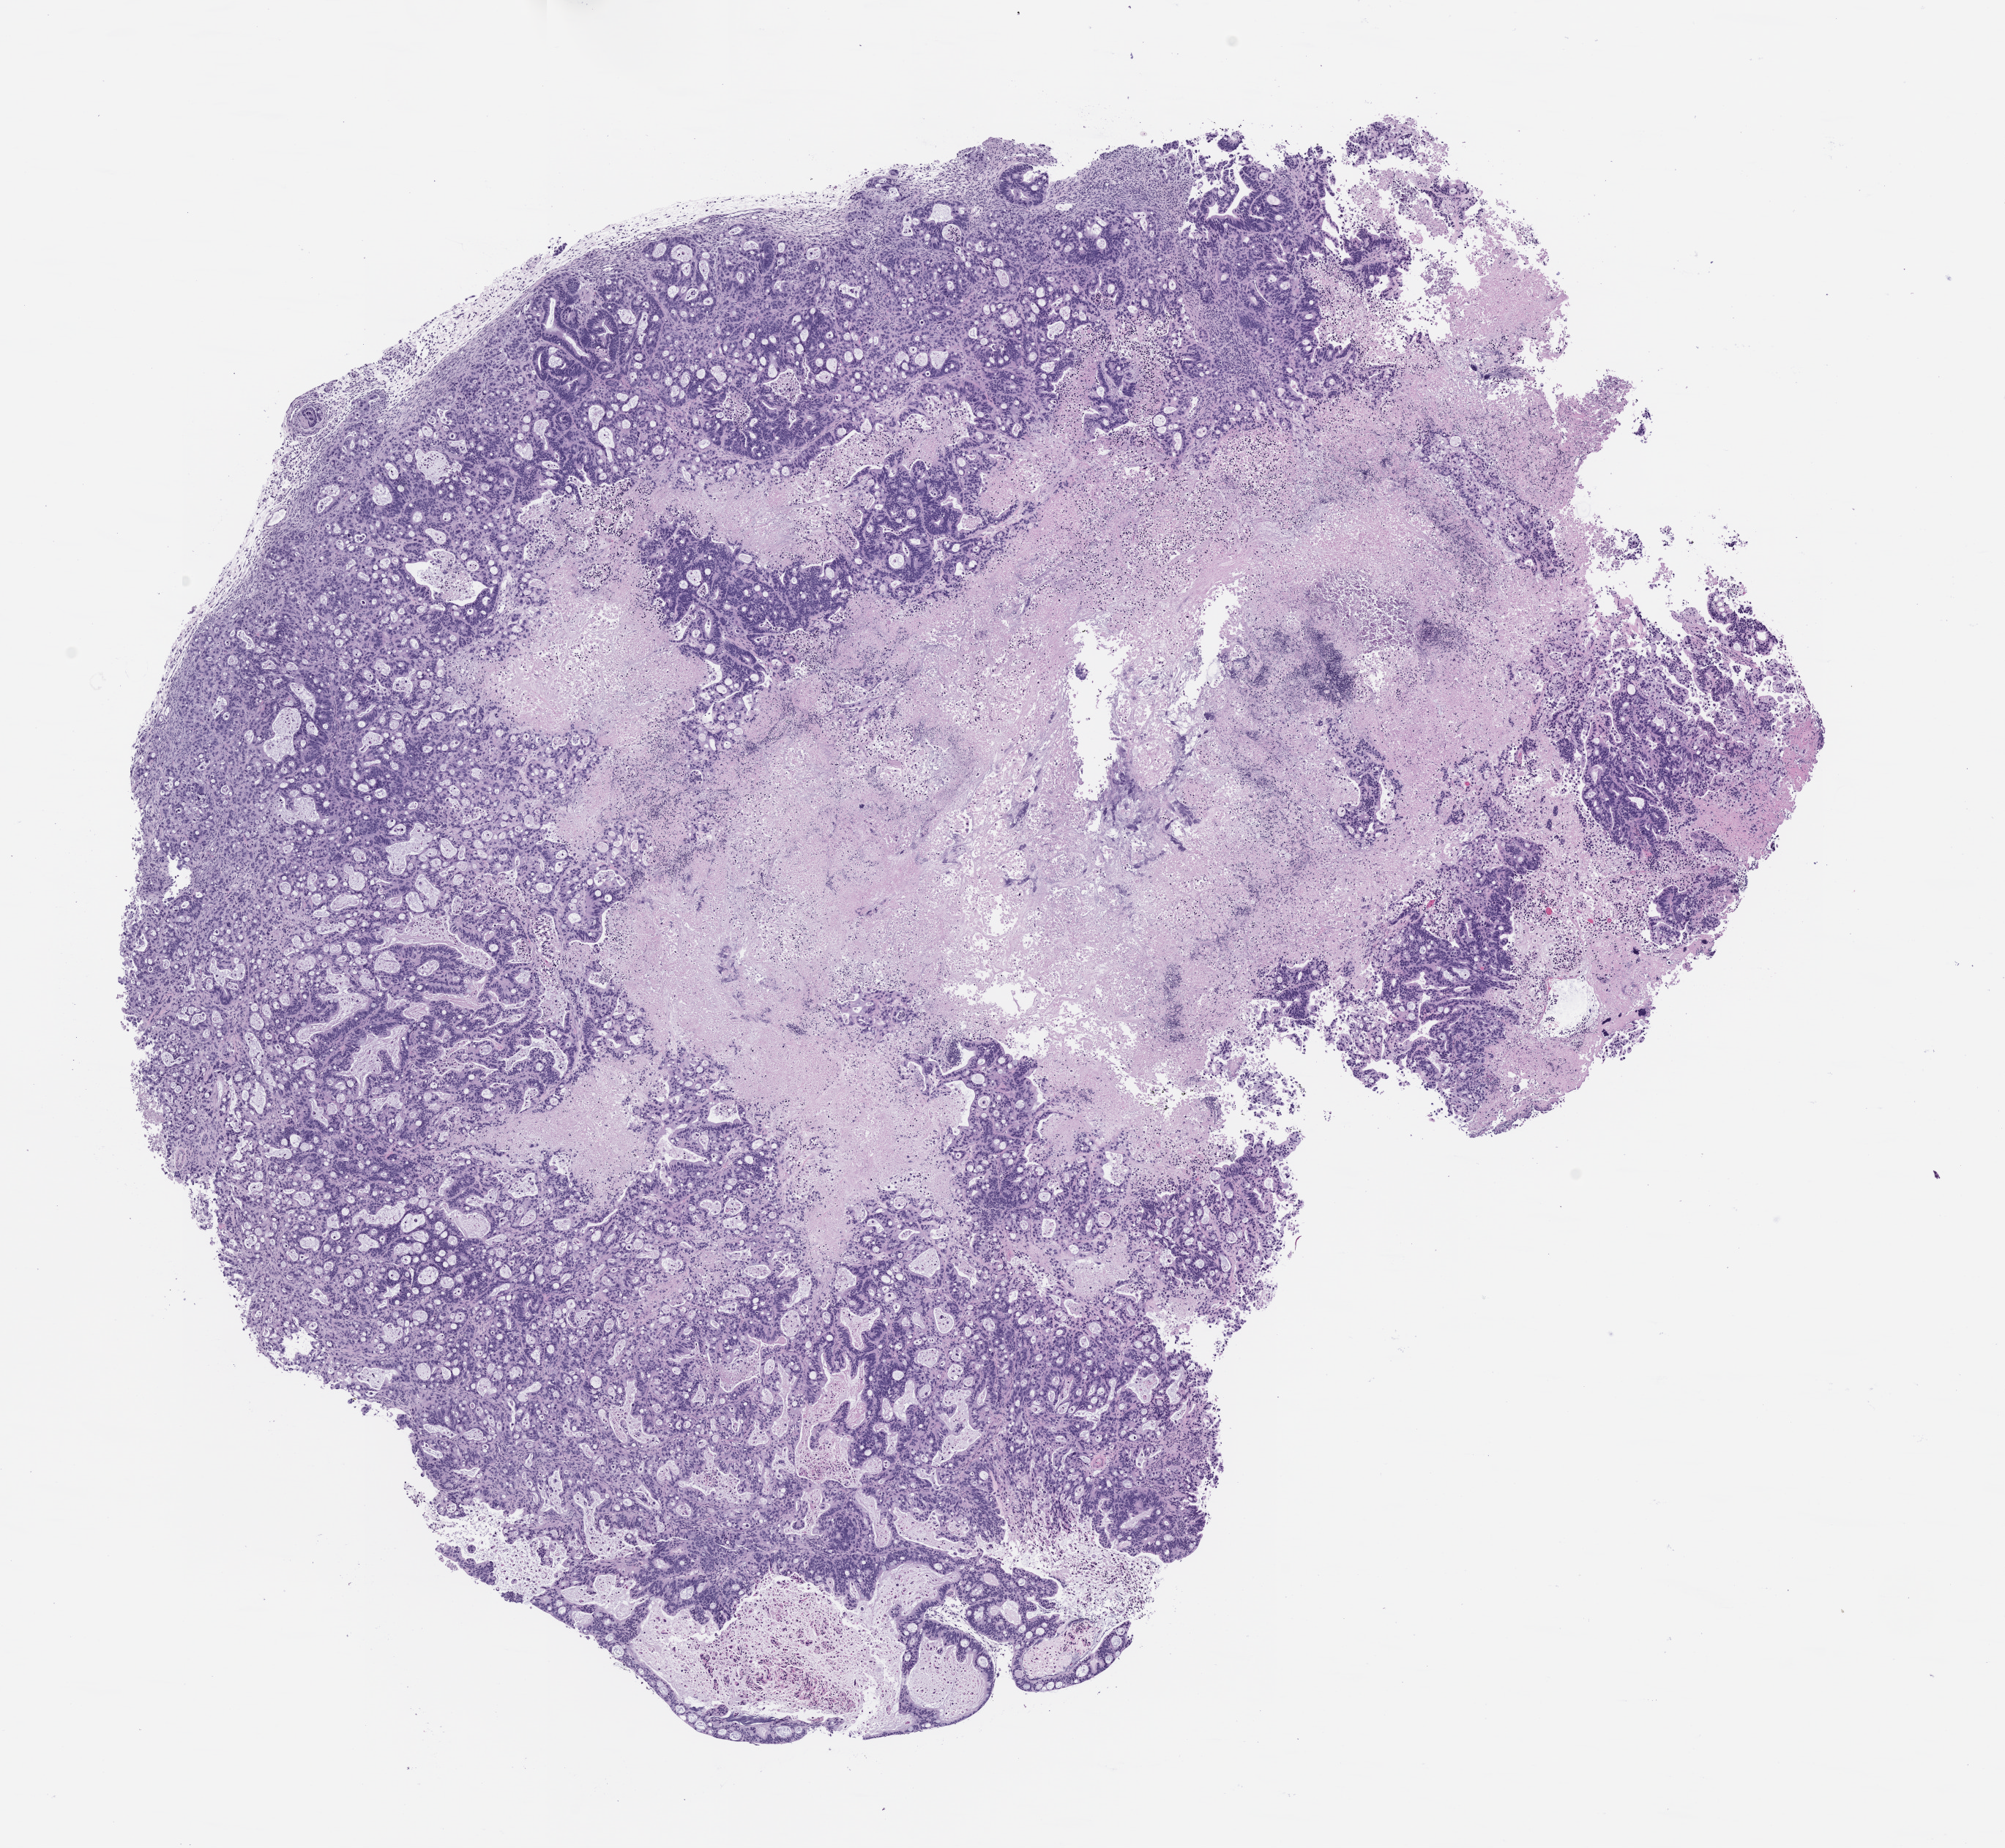
H&E whole-slide image of a patient-derived xenograft (PDX) tumor grown in a mouse, passage 2 — a low-resolution overview of the entire scanned area, about 11.0 x 10.2 mm. Formalin-fixed, paraffin-embedded (FFPE) tissue. Originating tumor site category: pancreas.
Originating patient diagnosis: Pancreatic Adenocarcinoma.